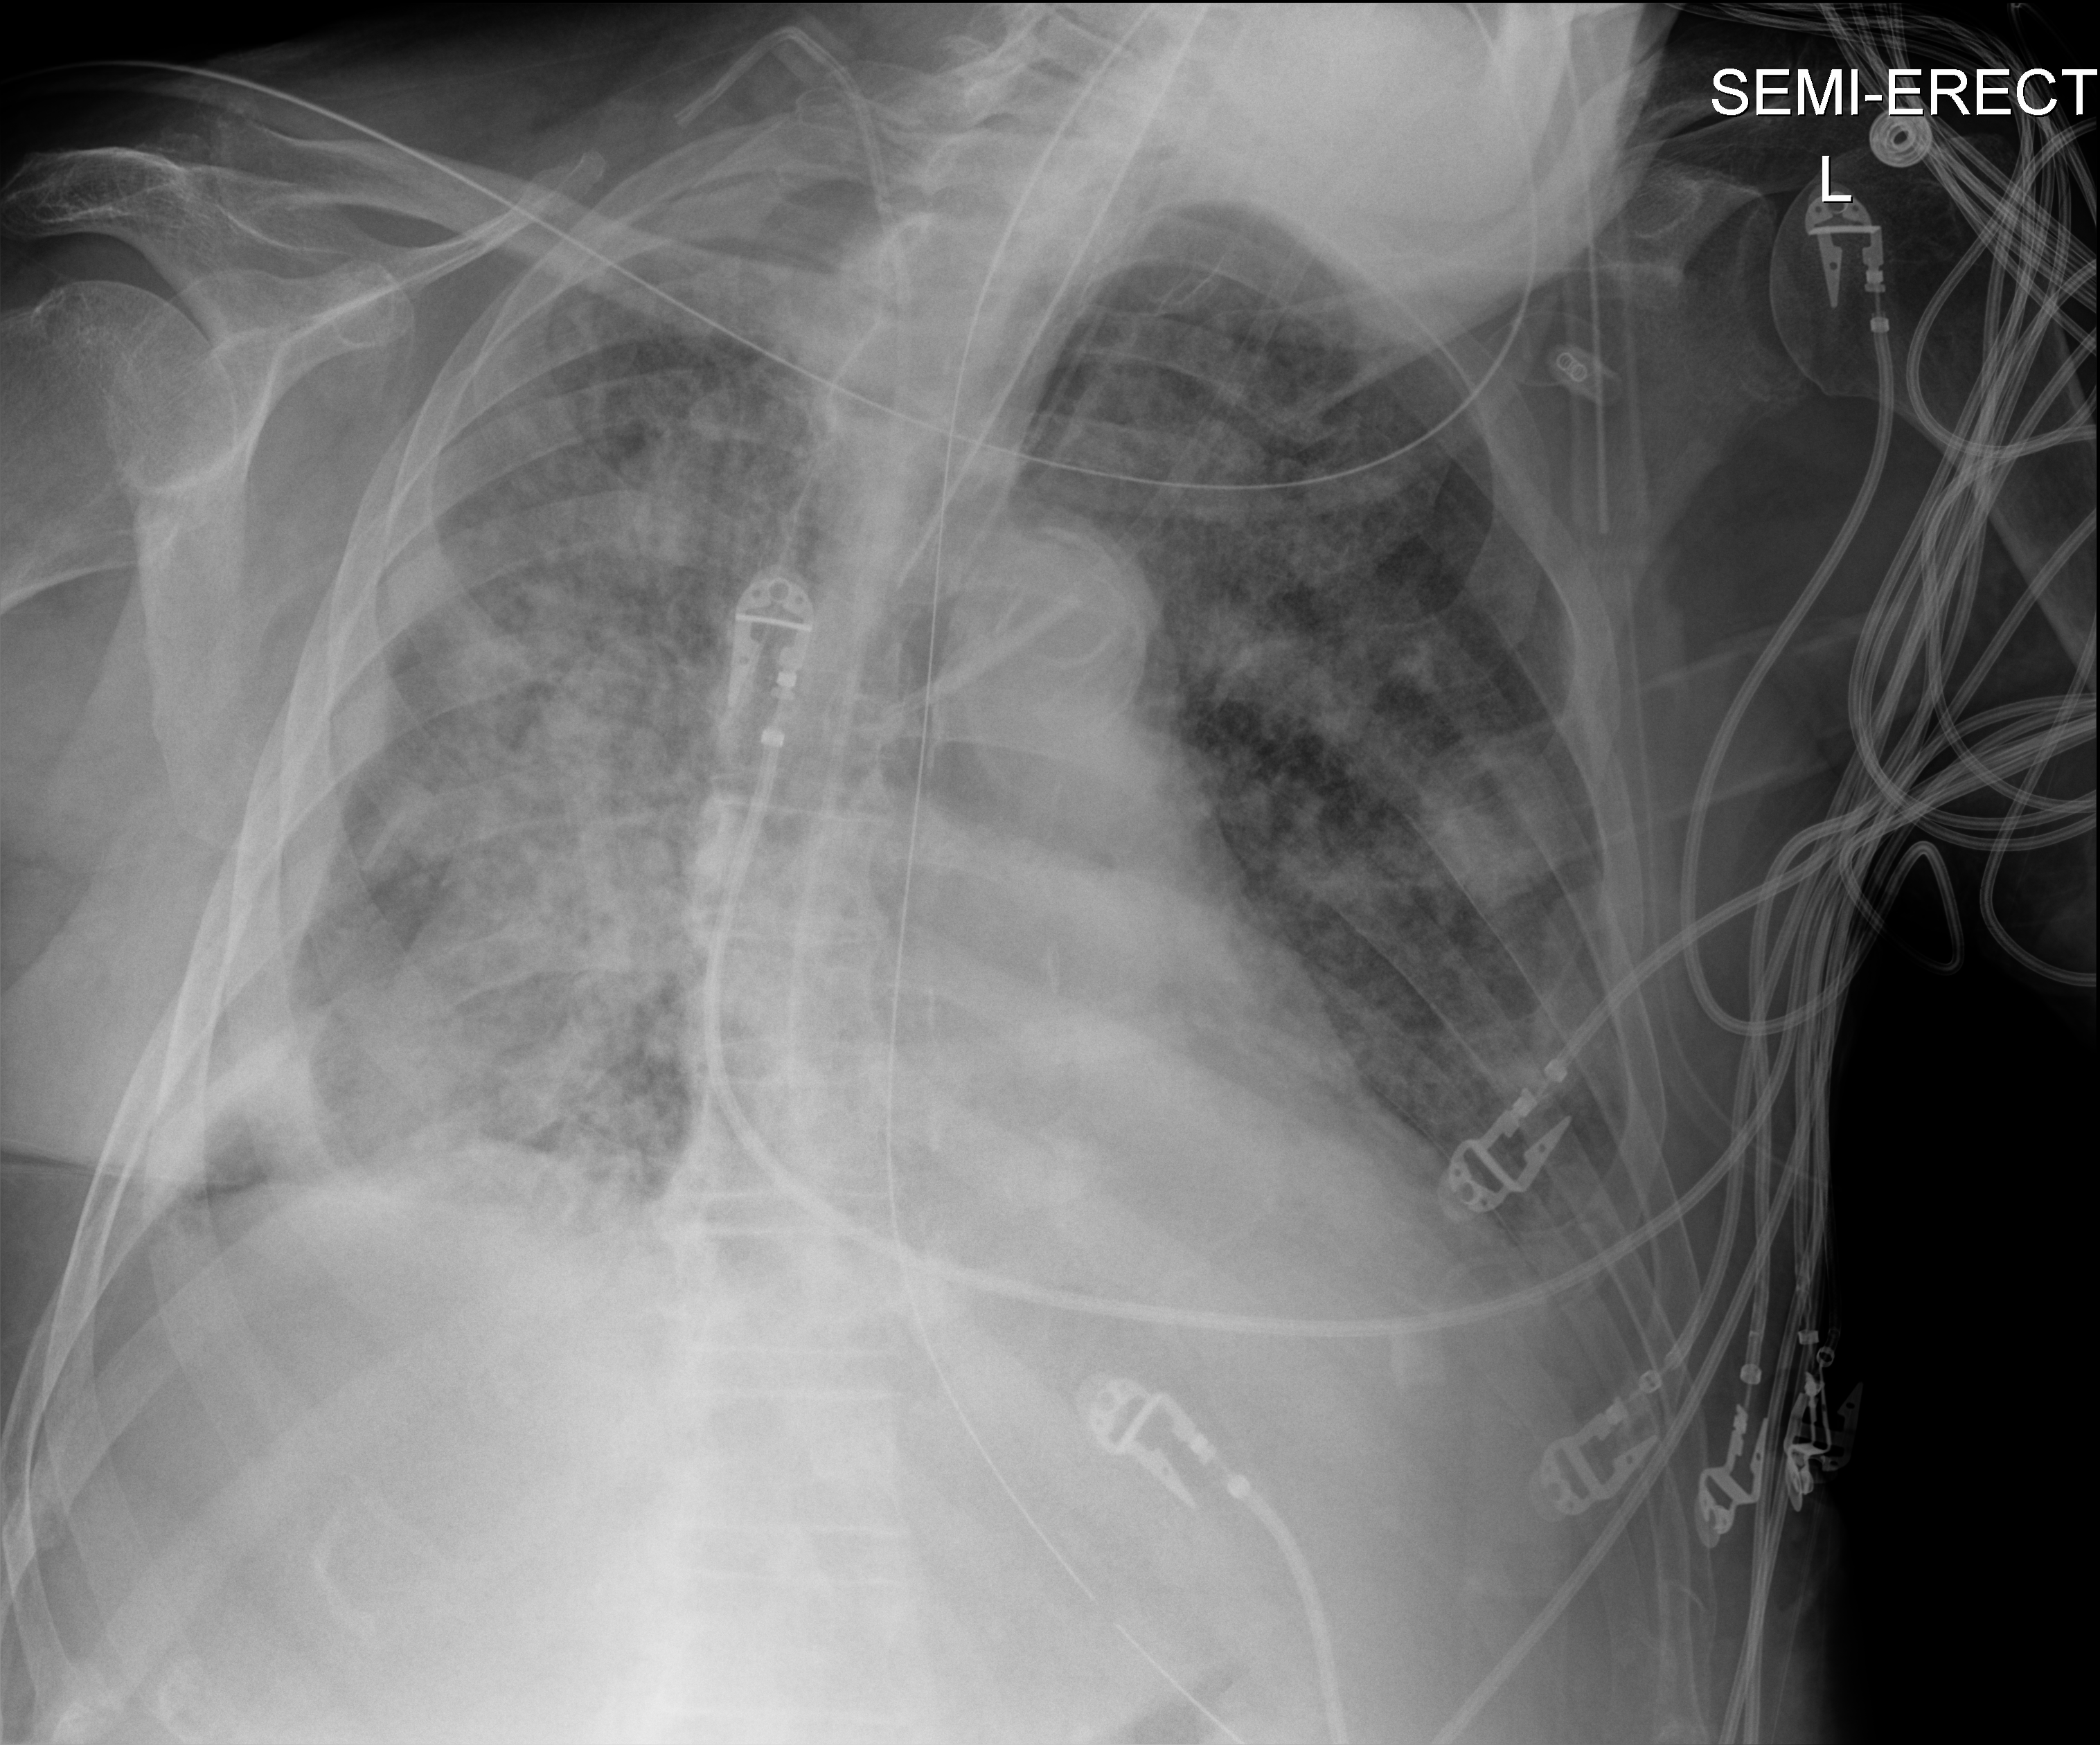
Portable chest radiograph, anteroposterior (AP) projection. Male patient hospitalised with COVID-19, age 75–90 years.
From the hospital-stay record, not from the radiograph (when in the stay this image was taken is not recorded):
- mechanically ventilated during this hospital stay: yes